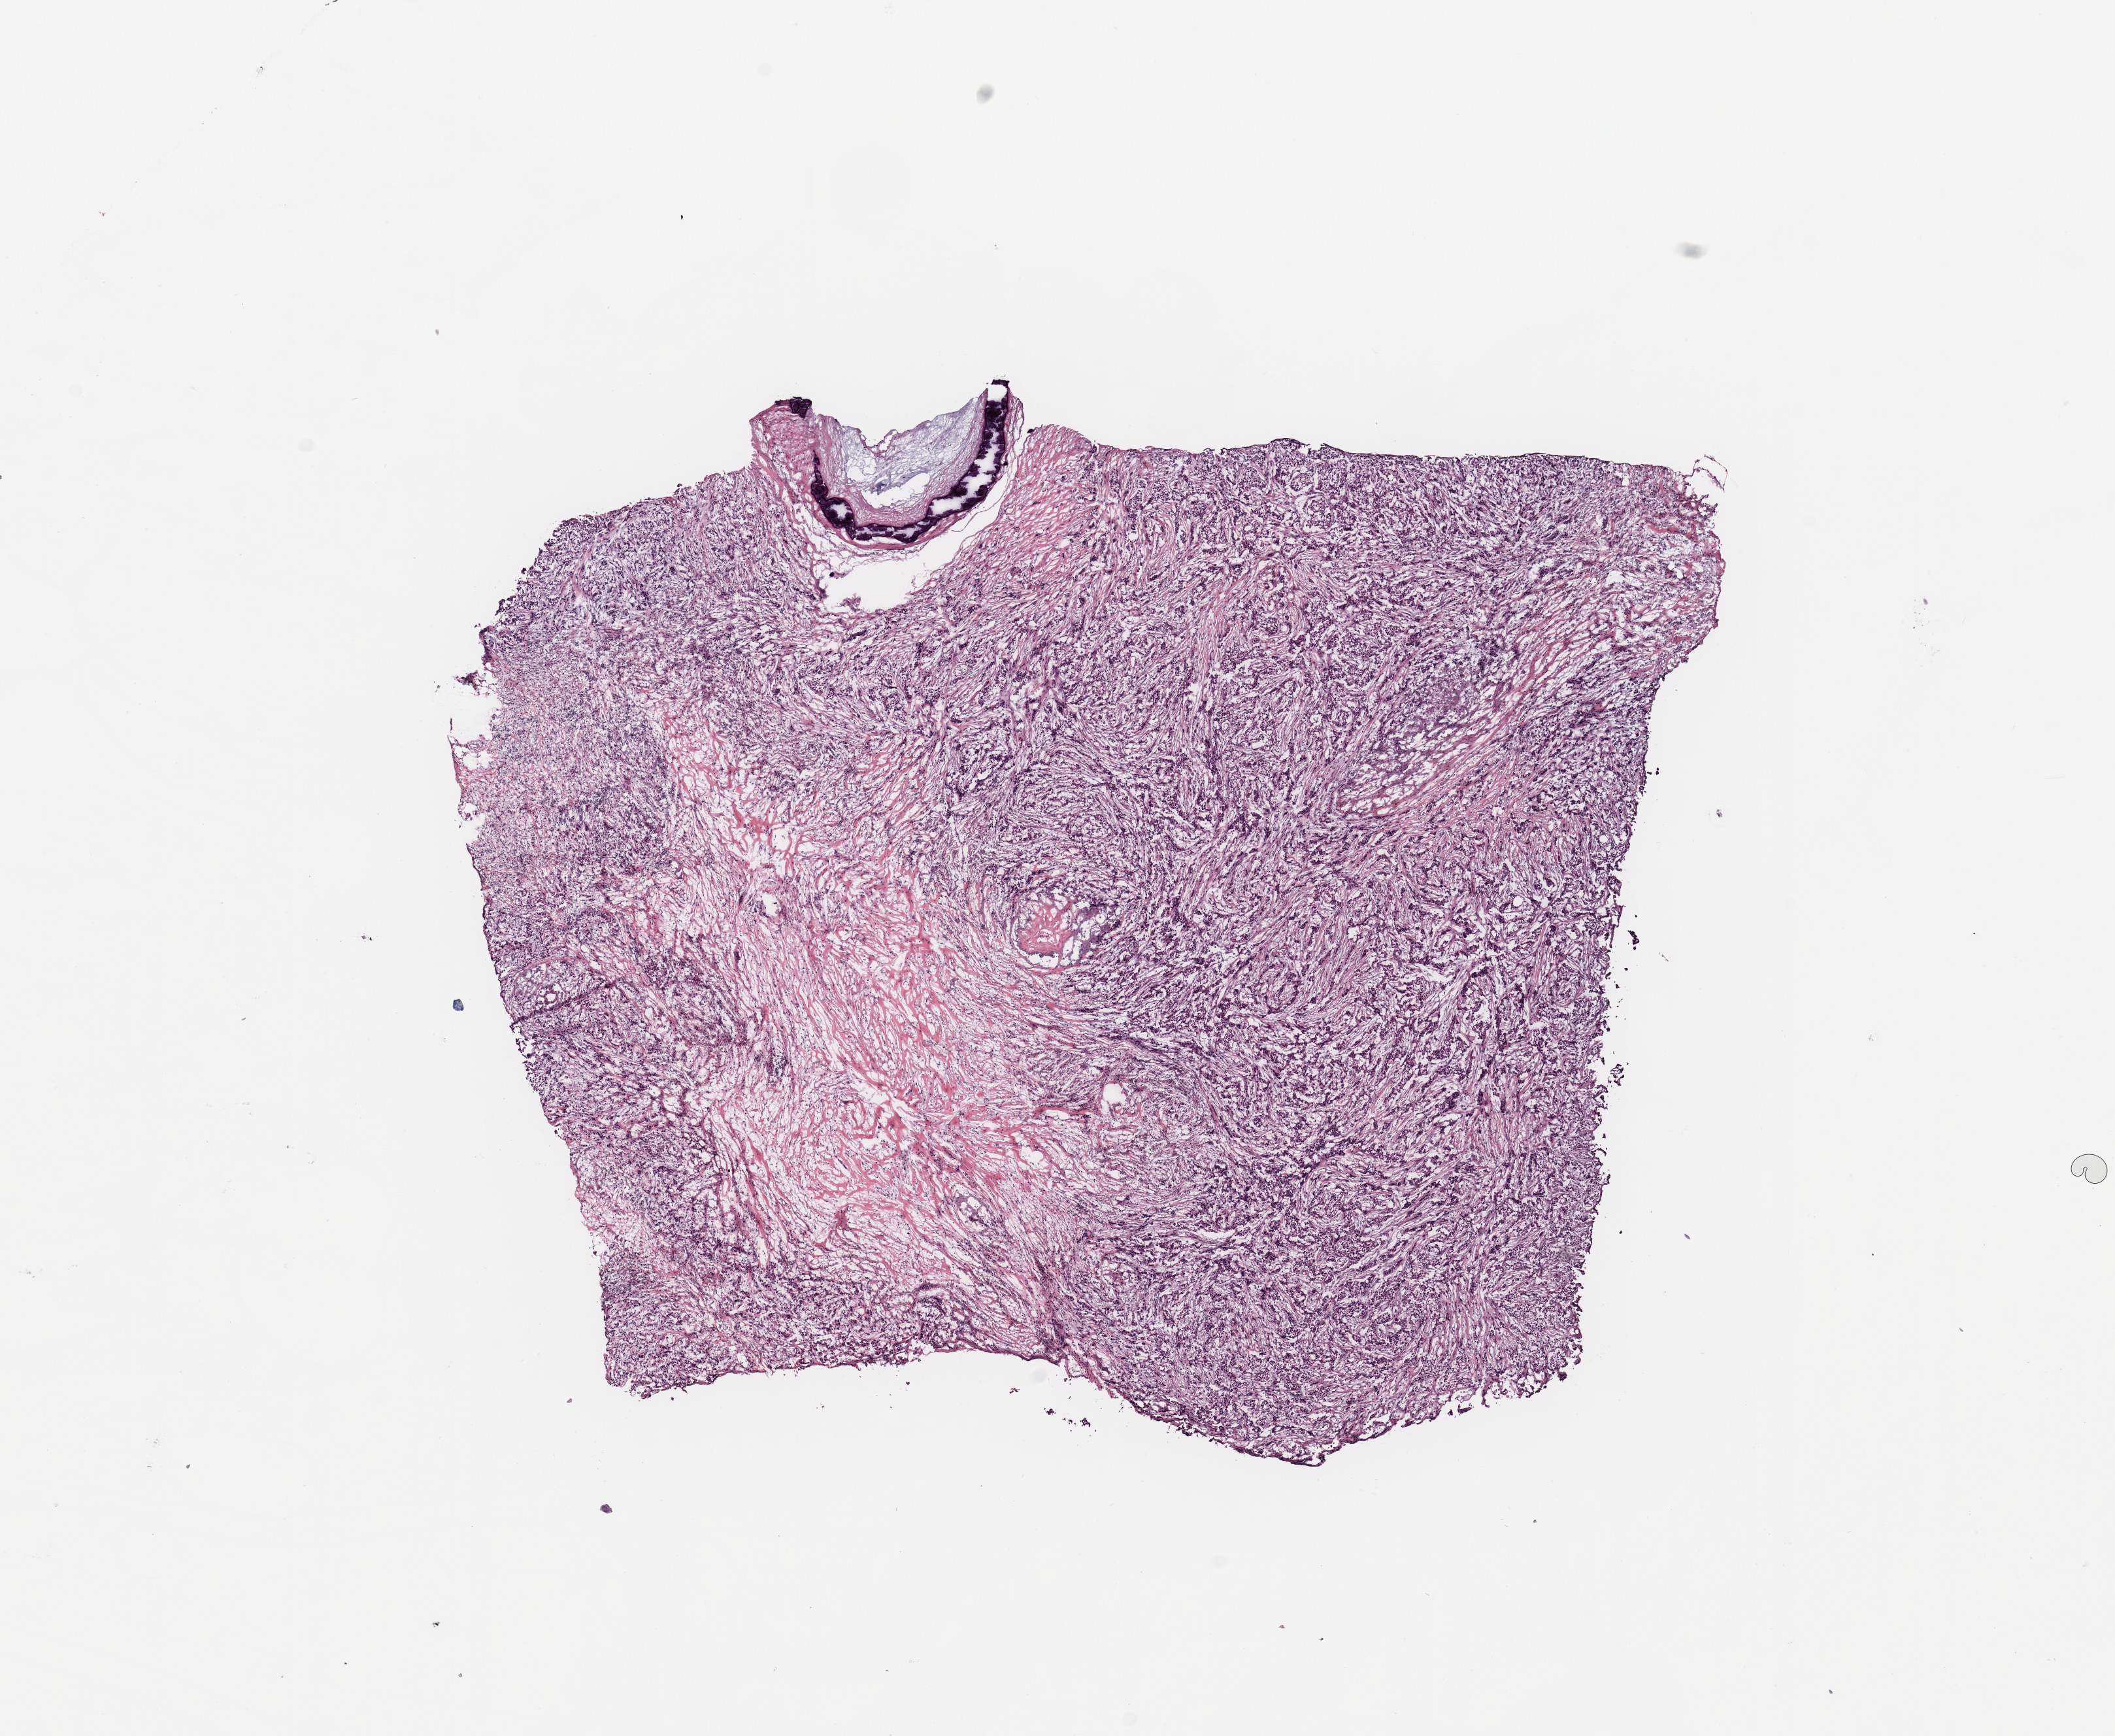
Hematoxylin and eosin (H&E) stained whole-slide image — shown as a low-resolution overview of the whole scanned area (about 12.8 x 10.5 mm). Patient: female, age 86 years.
Specimen: tumour tissue sample, breast.